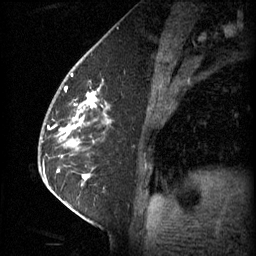
Breast MRI (dynamic contrast-enhanced), one sagittal slice; 3 images stored at this slice position (order not interpretable as contrast timing); 1.5 T; TE 4.2 ms, TR 11 ms; 2 mm slice thickness; 256 × 256 image matrix, field of view 180 × 180 mm. Patient: female, 62 years.
Annotated regions visible in this slice (semi-automatic segmentation, software-assisted and operator-edited):
- analysis volume of interest (the breast-tissue region the enhancement analysis was run in; not a lesion): bounding box <55,72,113,135> (left, top, right, bottom; pixels)
- tumour enhancement mask (voxels above the 70 % enhancement threshold inside the analysis volume of interest): <62,92,98,135>